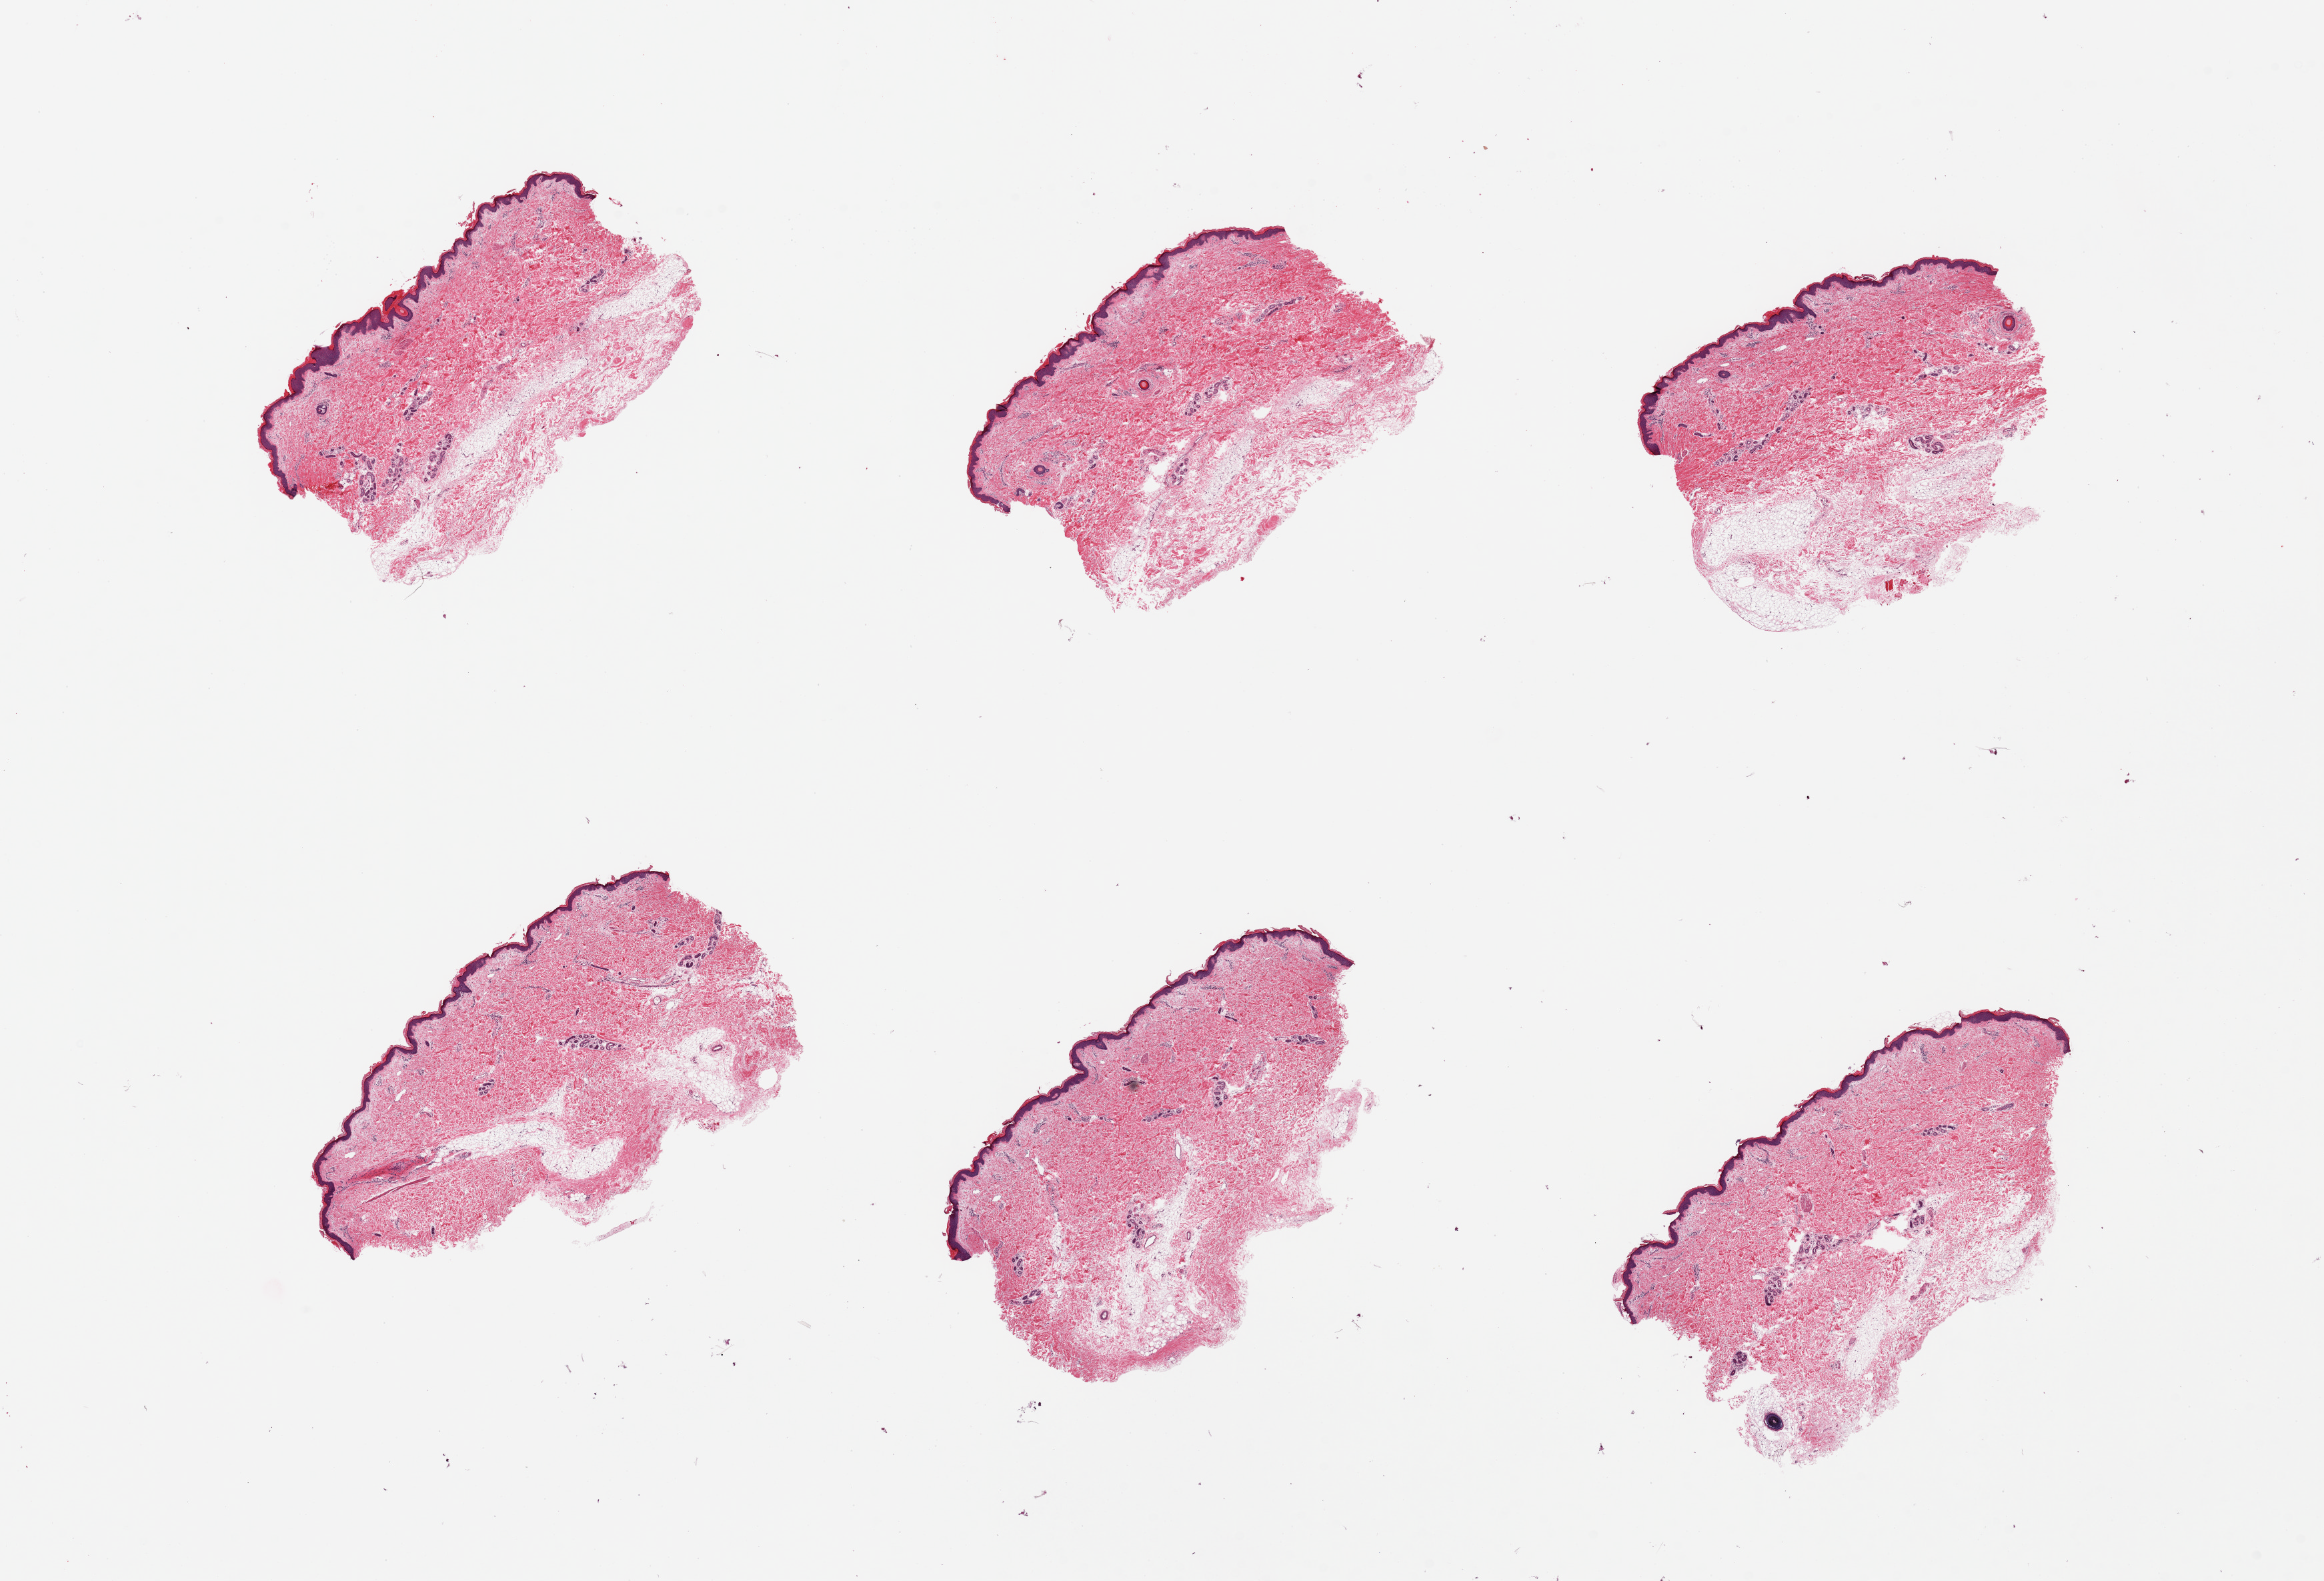
H&E whole-slide image, whole scanned area (about 27.6 x 18.8 mm) shown as a low-resolution overview.
Specimen: PAXgene-fixed paraffin-embedded (PFPE) section; sampled site (target tissue): skin of lower leg; donor tissue sample.